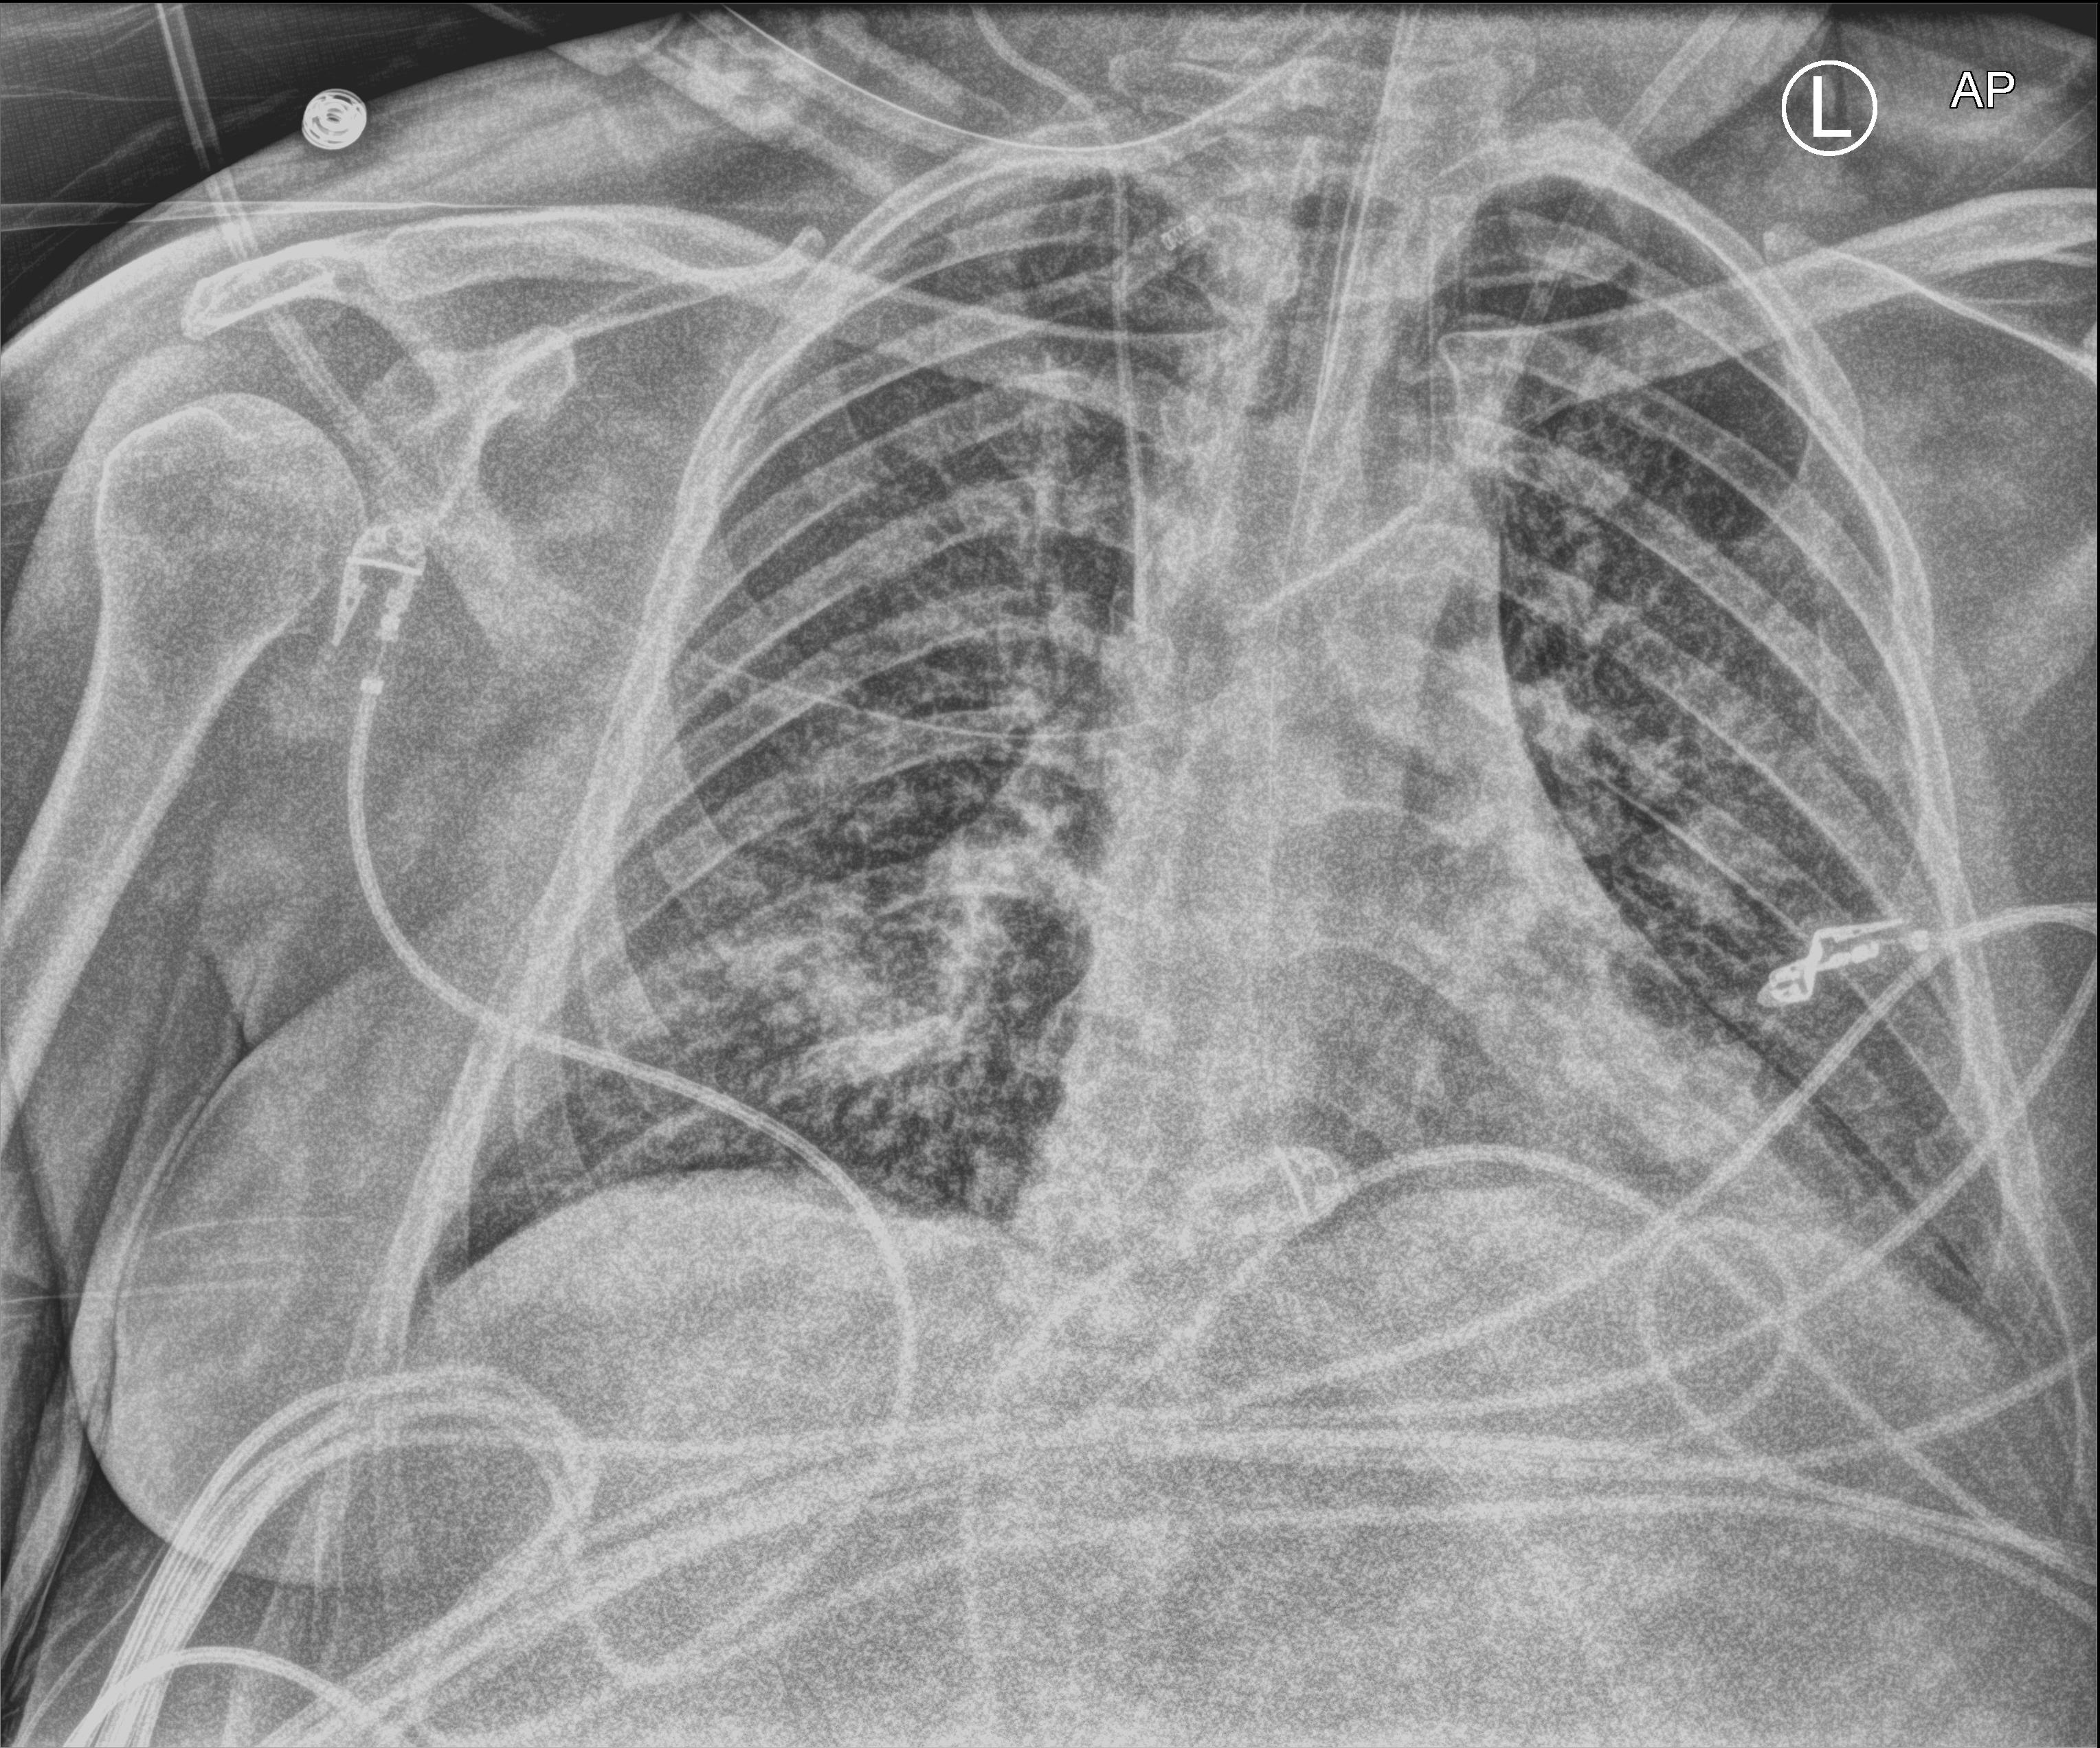
Bedside chest radiograph (computed radiography). Male patient hospitalised with COVID-19, age 18–59 years.
Hospital-stay facts (about this admission, not read from this image; timing relative to this image not recorded):
- COPD (admission record): no
- admitted to intensive care during this hospital stay: yes